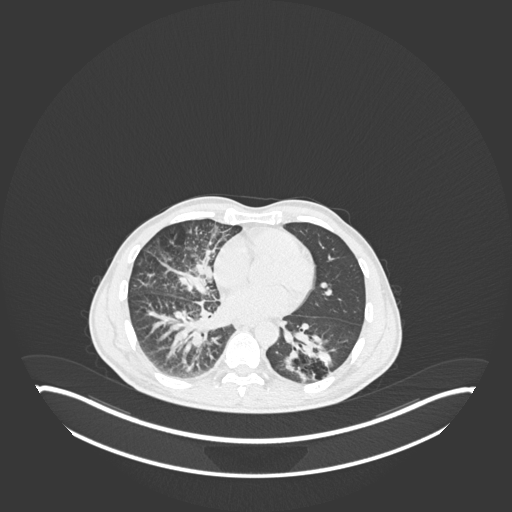
Chest CT, one axial slice; position 101 of 237 along the scan axis; reconstruction kernel B30f; 120 kVp; lung window (W 1500 / L -600 HU); 1 mm slice thickness; 512 × 512 image matrix, field of view 500 × 500 mm. Patient: male, 49 years. Case-level facts recorded for this patient, not image findings: clinical TNM (as recorded): T2b N1 M0.
Annotated regions visible in this slice (rectangle marked by the reading radiologist):
- lung tumour (recorded histology: adenocarcinoma): box from (x=284, y=330) to (x=340, y=383) px